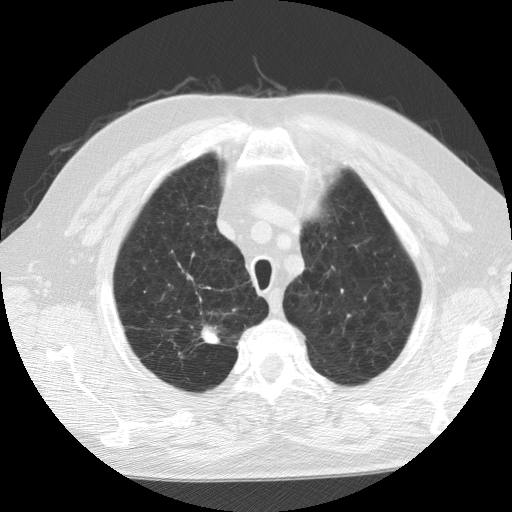
Axial slice from a low-dose chest CT screening exam, second screening round (one year after baseline), lung window (W 1500 / L -600 HU). Male, age 64 years at enrolment.
- Expert reader's lesion annotation, bounding box (x1, y1, x2, y2) in pixels: (184, 318, 235, 358).
- The screening reader recorded 2 non-calcified nodules or masses ≥4 mm on this exam; which of them this box marks is not recorded.
- Official screen result: positive, other.